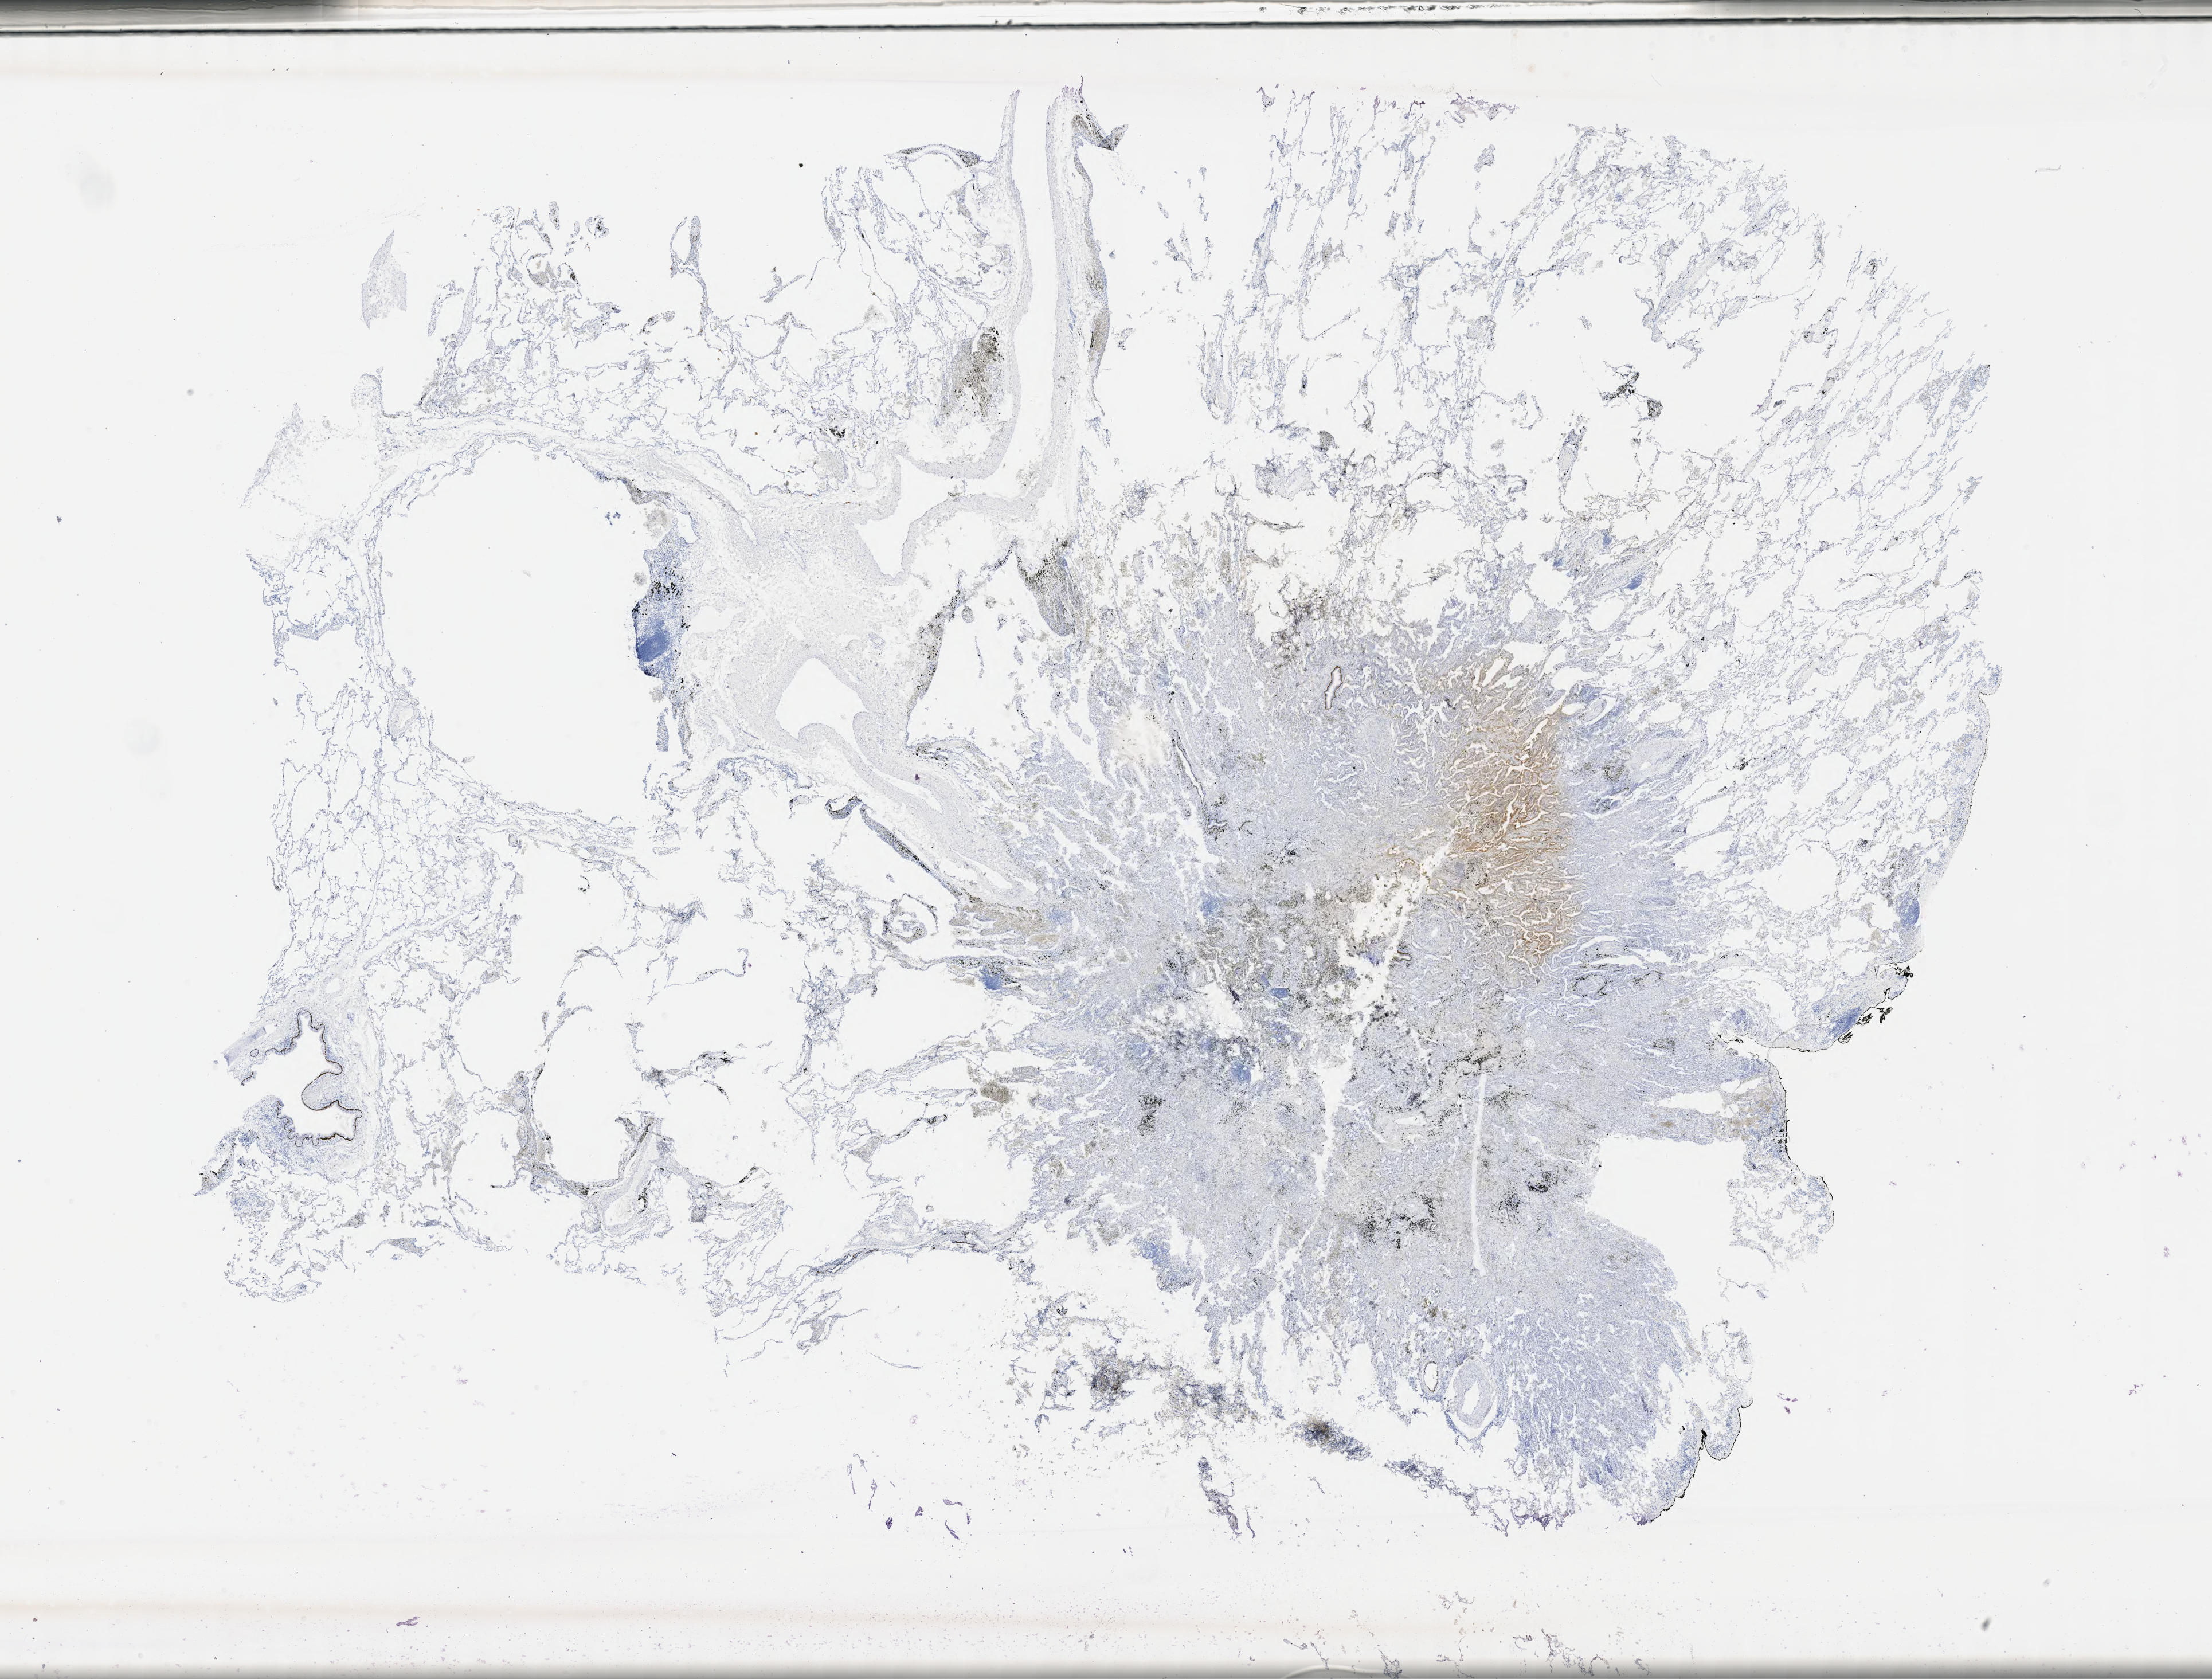
Whole-slide image, immunohistochemical stain for p40 — low-resolution overview of the scanned area, about 31.2 x 23.7 mm. Tumor tissue. Anatomic site: lung. Patient sex: male.
• histologic diagnosis: Mucinous adenocarcinoma